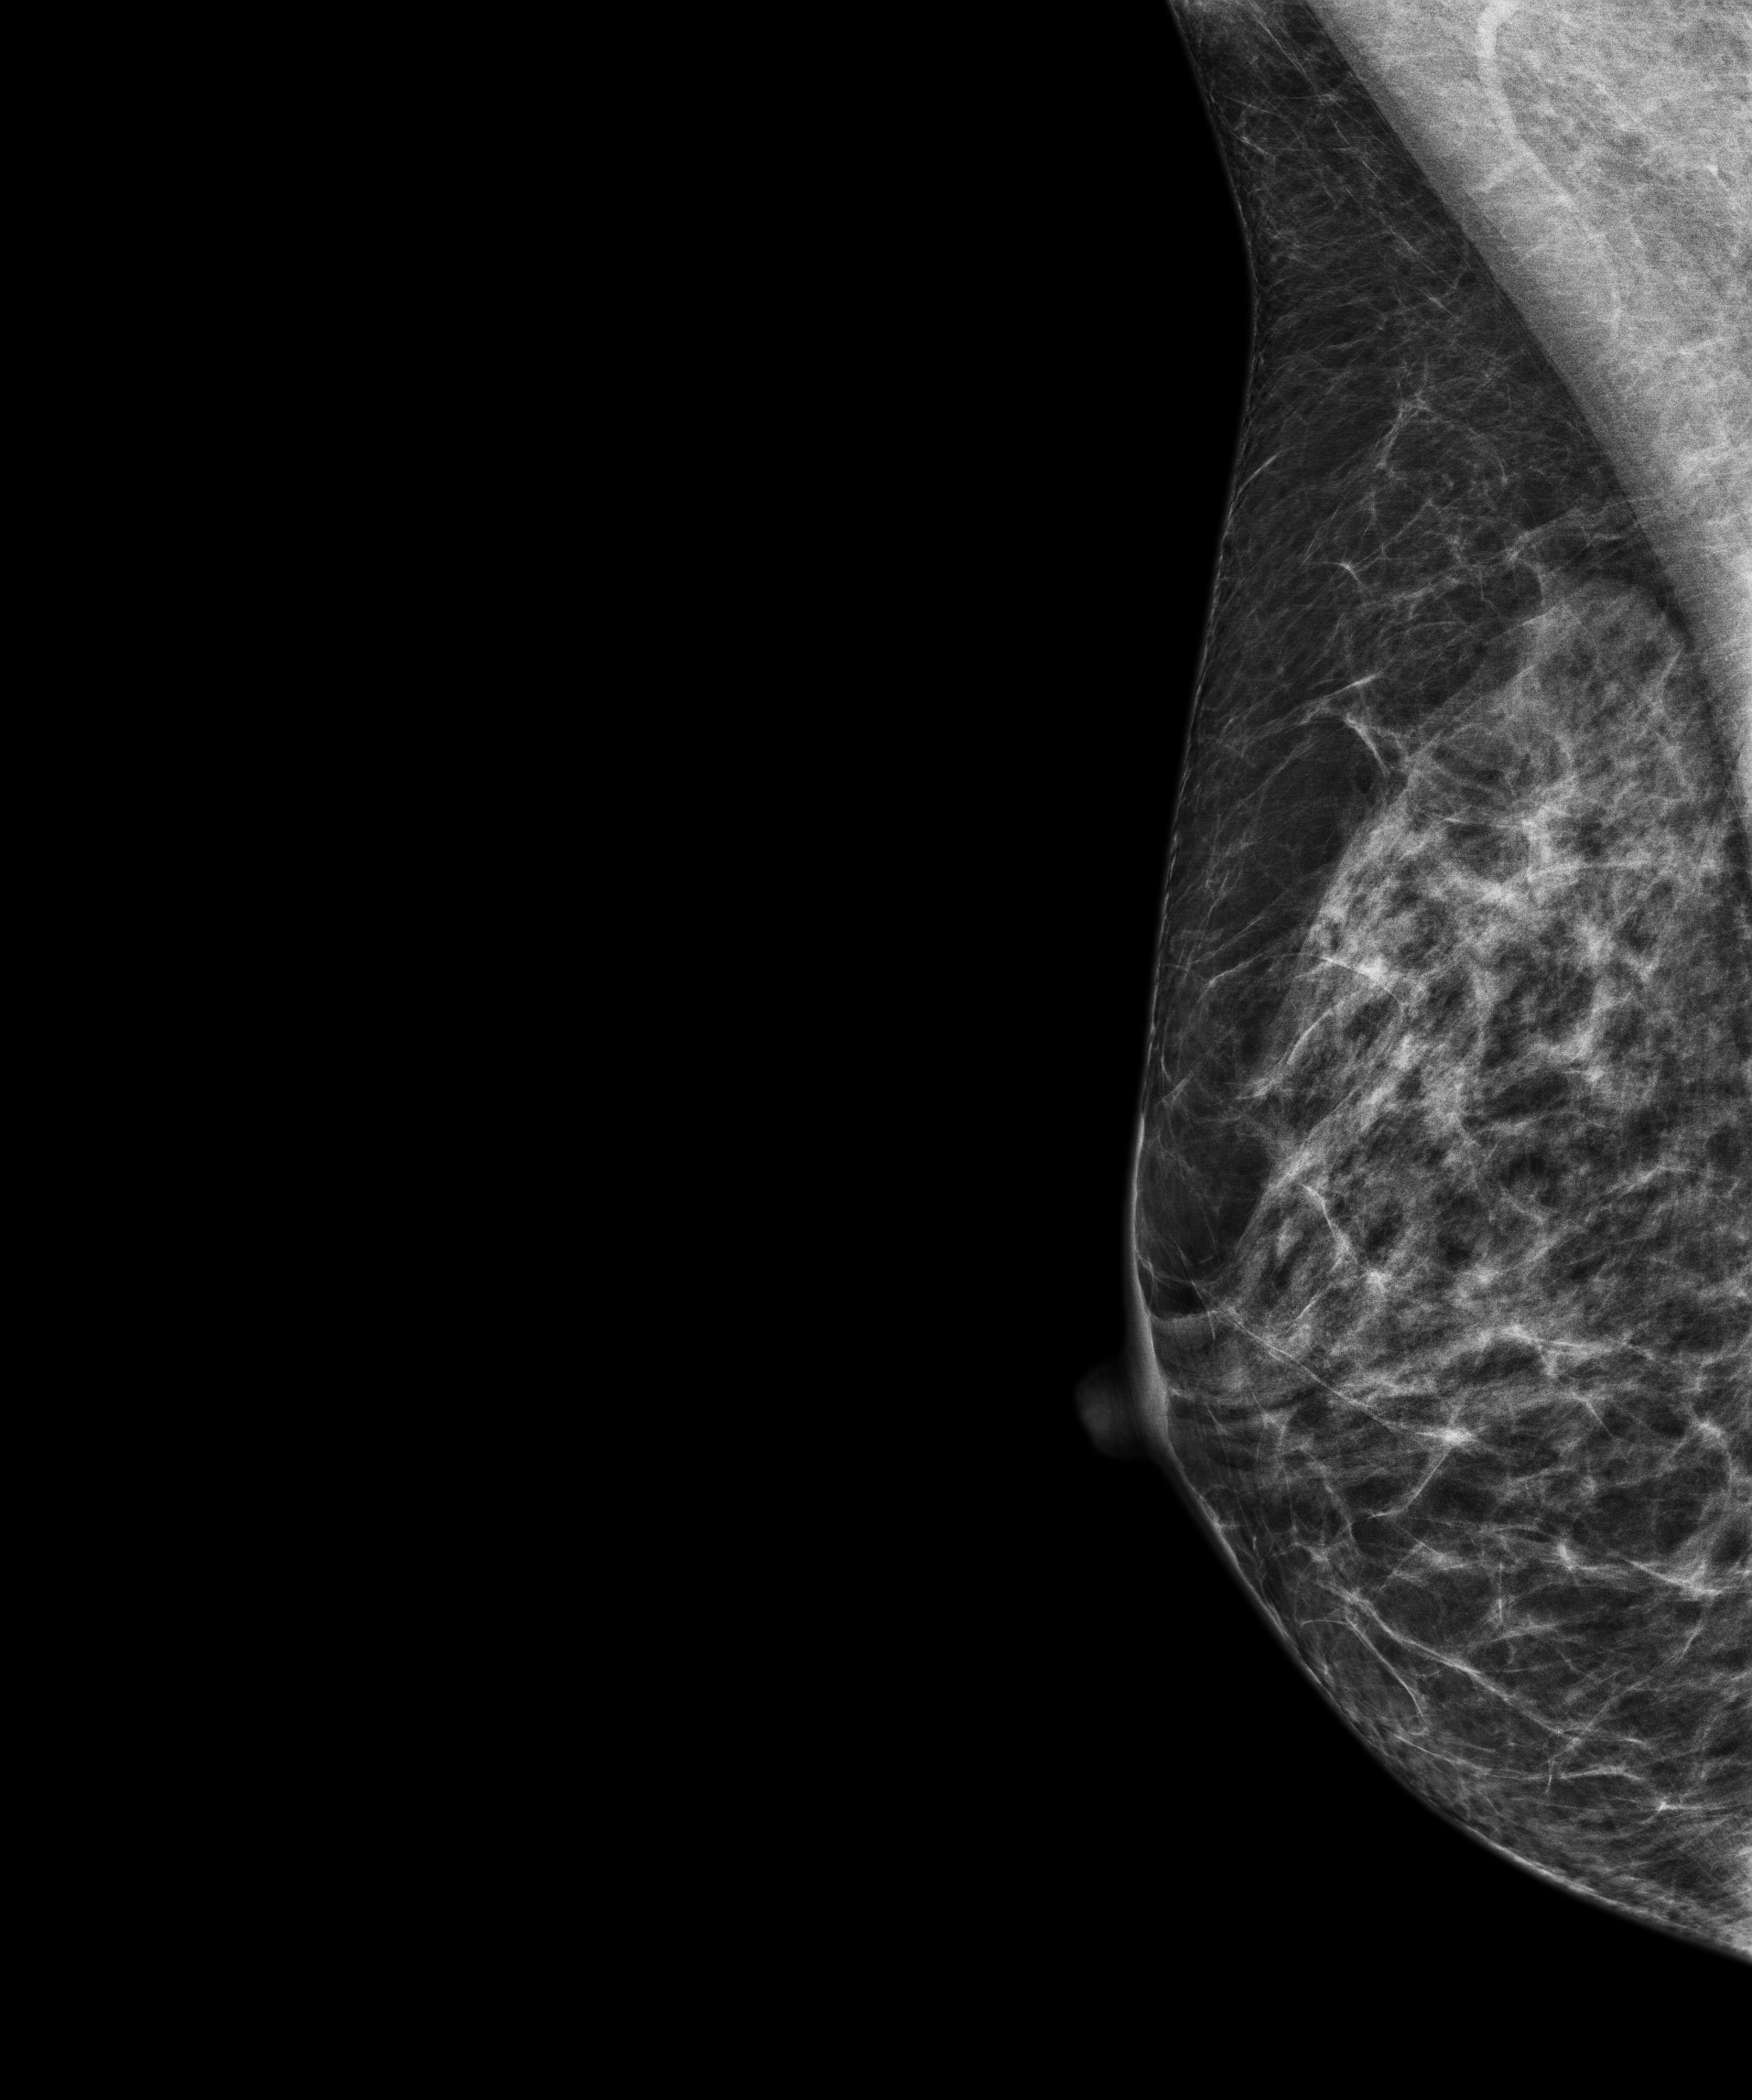
Annual screening mammography examination; system: Senographe Pristina. Patient aged 62 years (female).
Image type: full-field digital mammogram. Breast: right. Projection: mediolateral oblique (MLO) view.